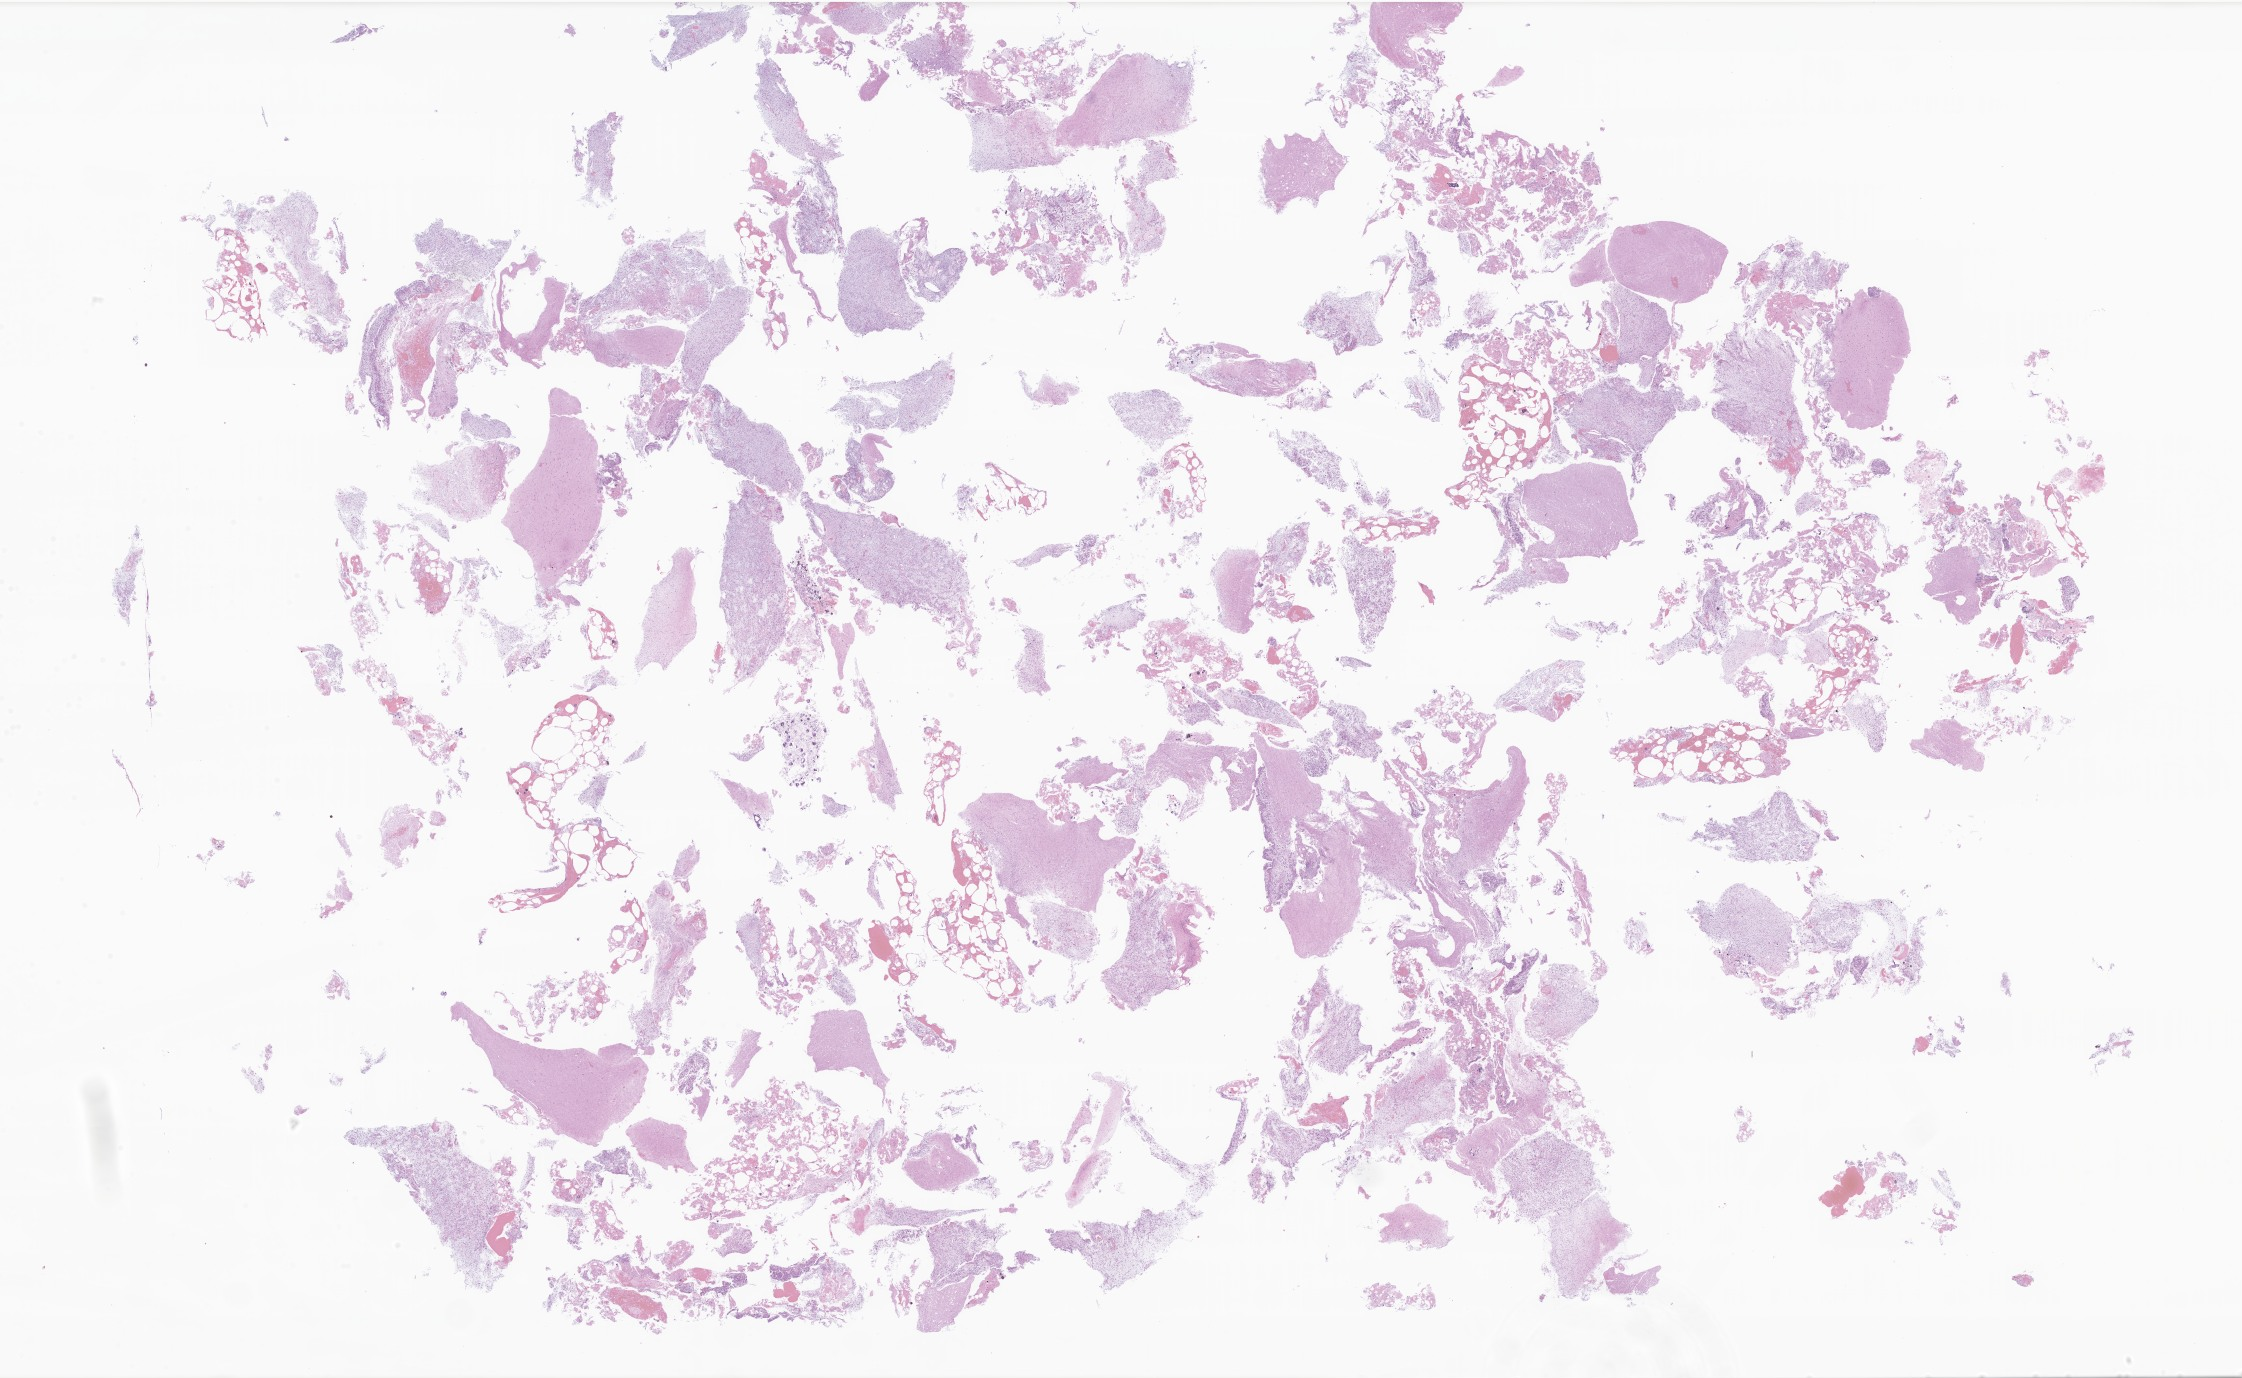
H&E whole-slide image of tumor tissue from the brain stem, shown as a low-resolution overview of the whole scanned area (about 37.8 x 23.2 mm). Formalin-fixed, paraffin-embedded (FFPE) tissue. Patient: female, age 205 months (17 years 1 month).
Diagnosis: Glioma, malignant.